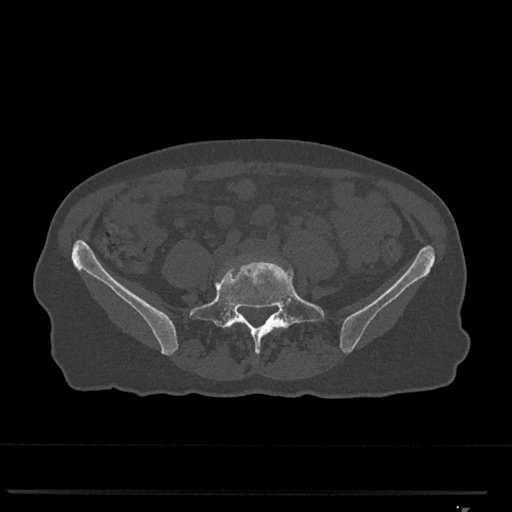
CT including the spine, one axial slice; slice 162 of 793 in the series (ordered by position); 120 kVp; bone window (W 1800 / L 400 HU); 0.5 mm slice thickness; 512 × 512 image matrix. Female patient, age 62 years. Case-level facts recorded for this patient, not image findings: primary cancer: renal.
Annotated regions visible in this slice (semi-automatic segmentation, software-assisted and operator-edited):
- L4 vertebra: box from (x=218, y=258) to (x=257, y=325) px
- L5 vertebra: (x=190, y=257)–(x=325, y=354)